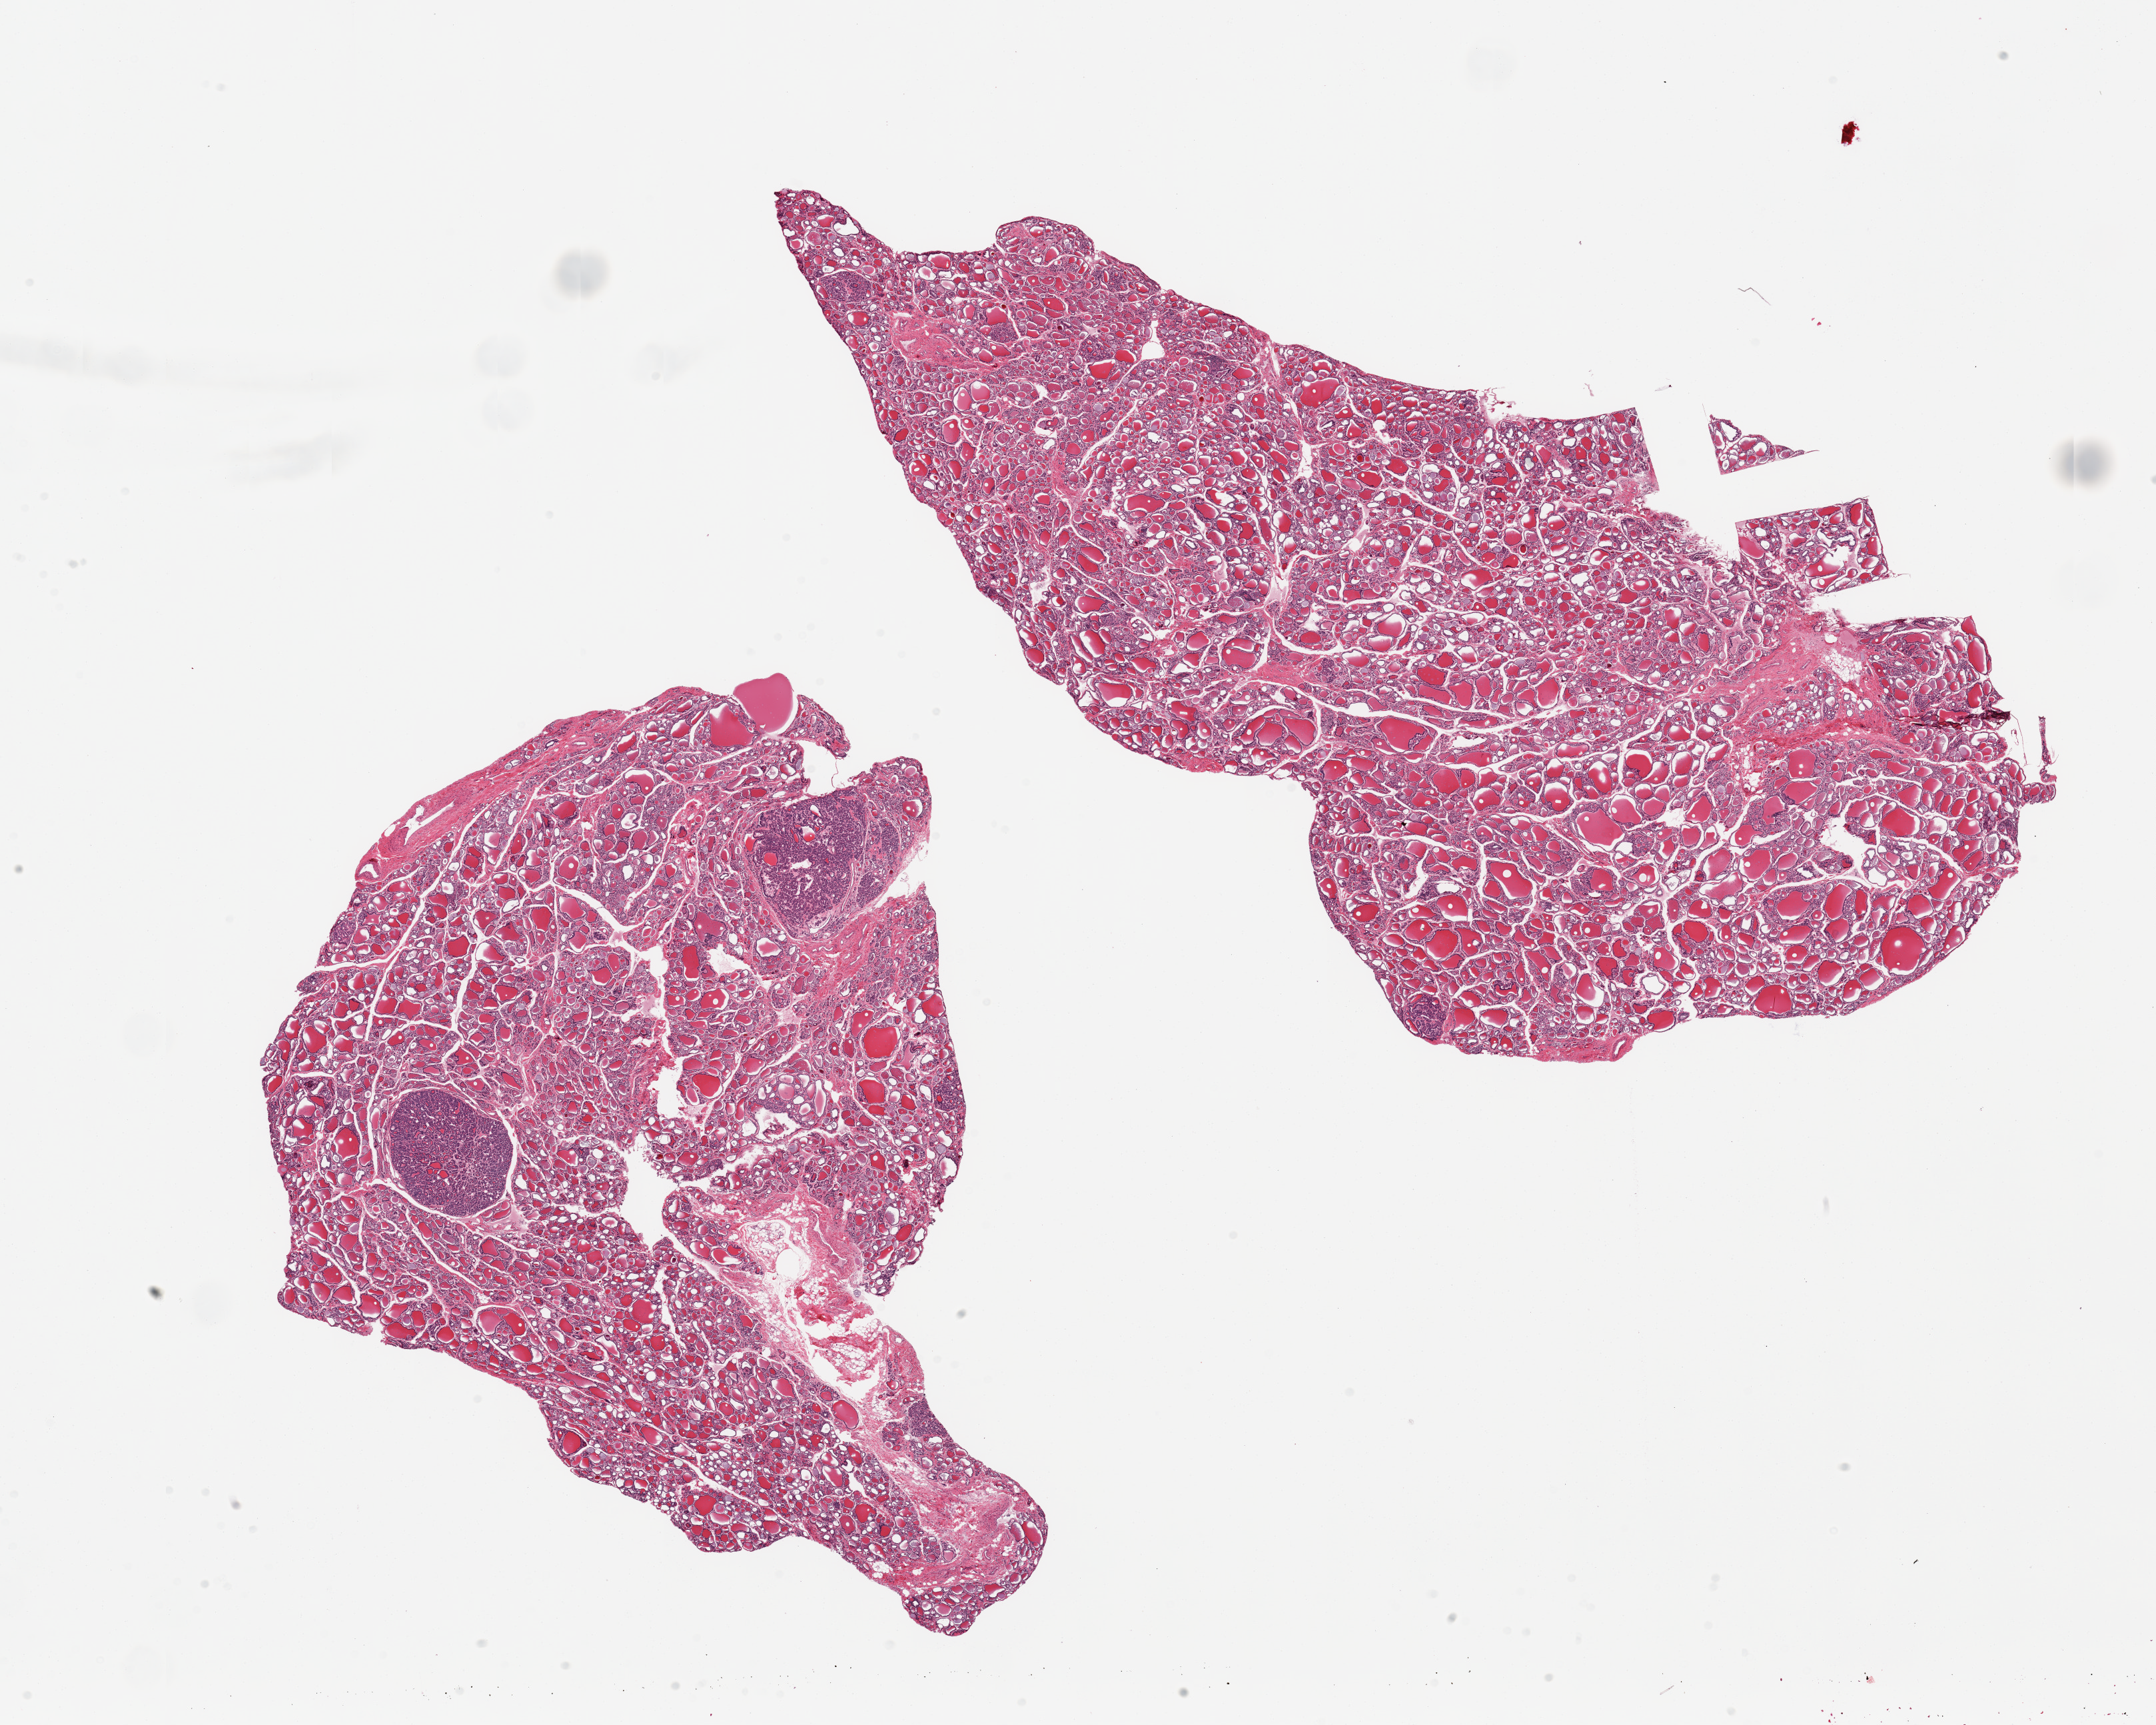
Hematoxylin and eosin (H&E) whole-slide image, a low-resolution overview of the entire scanned area, about 25.6 x 20.5 mm. PAXgene-fixed paraffin-embedded (PFPE) section. Section of thyroid (target tissue). Donor tissue sample.
Reviewer comment on this tissue sample: 2 pieces; adenomatous nodules.